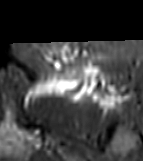
MRI of an extremity soft-tissue mass, one axial slice; position 48 of 81 along the scan axis; STIR; MR volume resampled by the dataset authors to the PET/CT grid (not the native acquisition matrix); 3.27 mm slice thickness; 143 × 161 image matrix. Female patient. Case-level facts recorded for this patient, not image findings: histological type: myxofibrosarcoma; grade: intermediate; site of the primary tumour: left thigh.
Annotated regions visible in this slice (expert contour drawn on MRI and transferred to this co-registered scan by the dataset authors):
- gross tumour volume including surrounding oedema: box from (x=24, y=65) to (x=121, y=107) px